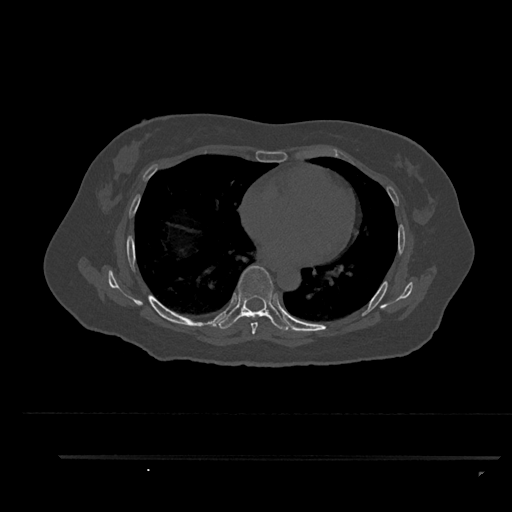
CT including the spine, one axial slice. Position 523 of 797 along the scan axis. Reconstruction kernel Br40s/3. 120 kVp. Bone window (W 1800 / L 400 HU). 0.5 mm slice thickness. 512 × 512 image matrix, field of view 408 × 408 mm. Female patient, age 44 years. From the clinical record (not read from this slice): primary cancer: renal; vertebrae with lytic lesions (as recorded): L1.
Annotated regions visible in this slice (semi-automatically segmented with operator editing):
- T6 vertebra: box from (x=250, y=317) to (x=258, y=335) px
- T7 vertebra: (x=218, y=266)–(x=291, y=331)